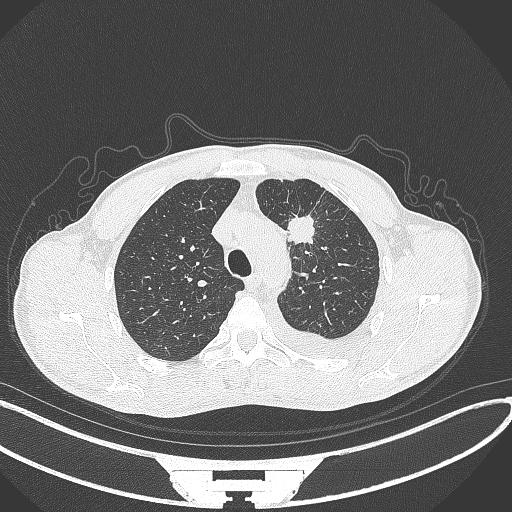
Chest CT, one axial slice; position 261 of 371 along the scan axis; 120 kVp; lung window (W 1500 / L -600 HU); 1 mm slice thickness; 512 × 512 image matrix, field of view 400 × 400 mm. Patient: male, 49 years. Case-level facts recorded for this patient, not image findings: clinical TNM (as recorded): T1c N1 M1.
Annotated regions visible in this slice (rectangle marked by the reading radiologist):
- lung tumour (recorded histology: adenocarcinoma): bounding box <289,210,320,250> (left, top, right, bottom; pixels)